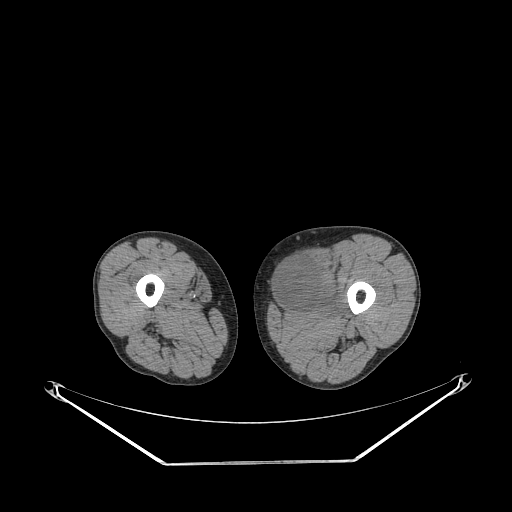
CT of an extremity soft-tissue mass (from a PET/CT study), one axial slice. Slice 230 of 267 in the series (ordered by position). Reconstruction kernel STANDARD. 140 kVp. Soft-tissue window (W 400 / L 40 HU). 3.75 mm slice thickness. 512 × 512 image matrix, field of view 500 × 500 mm. Male patient. Case-level facts recorded for this patient, not image findings: histological type: pleiomorphic liposarcoma; grade: high; site of the primary tumour: left thigh.
Structures marked on this image (expert contour drawn on MRI and transferred to this co-registered scan by the dataset authors):
- gross tumour volume including surrounding oedema: box from (x=276, y=256) to (x=344, y=318) px
- gross tumour volume (mass): (x=276, y=256)–(x=321, y=309)